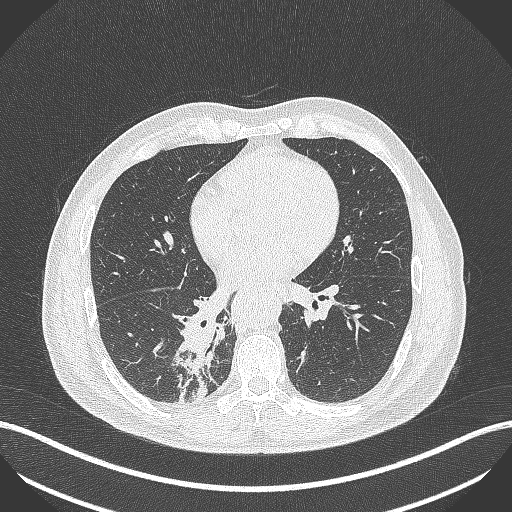
Chest CT, one axial slice. Slice 213 of 451 in the series (ordered by position). Reconstruction kernel B70f. Lung window (W 1500 / L -600 HU). 1 mm slice thickness. 512 × 512 image matrix, field of view 400 × 400 mm. Male patient, age 61 years. Case-level facts recorded for this patient, not image findings: clinical TNM (as recorded): T1 N0 M0; histopathological grade: G3.
Outlined on this slice (bounding box drawn by a radiologist):
- lung tumour (recorded histology: small cell carcinoma): bounding box (x1, y1, x2, y2) in pixels: (176, 311, 217, 403)